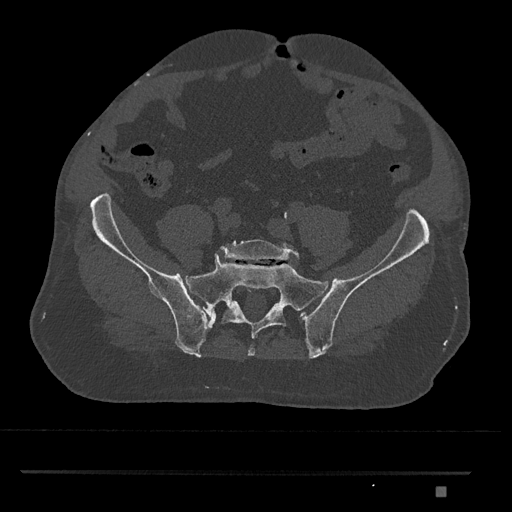
CT including the spine, one axial slice. Slice 508 of 1134 in the series (ordered by position). Reconstruction kernel Br40s/3. Bone window (W 1800 / L 400 HU). 512 × 512 image matrix, field of view 429 × 429 mm. Patient: male, 65 years. Case-level facts recorded for this patient, not image findings: primary cancer: prostate.
Structures marked on this image (semi-automatic segmentation, software-assisted and operator-edited):
- L5 vertebra: bounding box (x1, y1, x2, y2) in pixels: (218, 239, 299, 262)